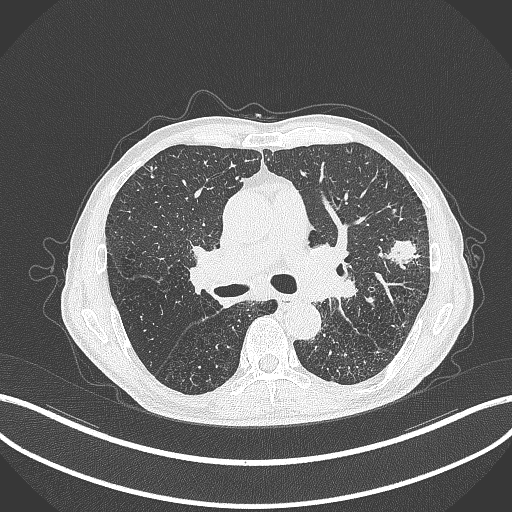
Chest CT, one axial slice; slice 253 of 463 in the series (ordered by position); reconstruction kernel B70f; lung window (W 1500 / L -600 HU); 1 mm slice thickness; 512 × 512 image matrix, field of view 400 × 400 mm. Male patient, age 74 years. From the clinical record (not read from this slice): clinical TNM (as recorded): T2a N1 M0.
Structures marked on this image (bounding box drawn by a radiologist):
- lung tumour (recorded histology: adenocarcinoma): bounding box [x1, y1, x2, y2] px = [374, 232, 419, 268]